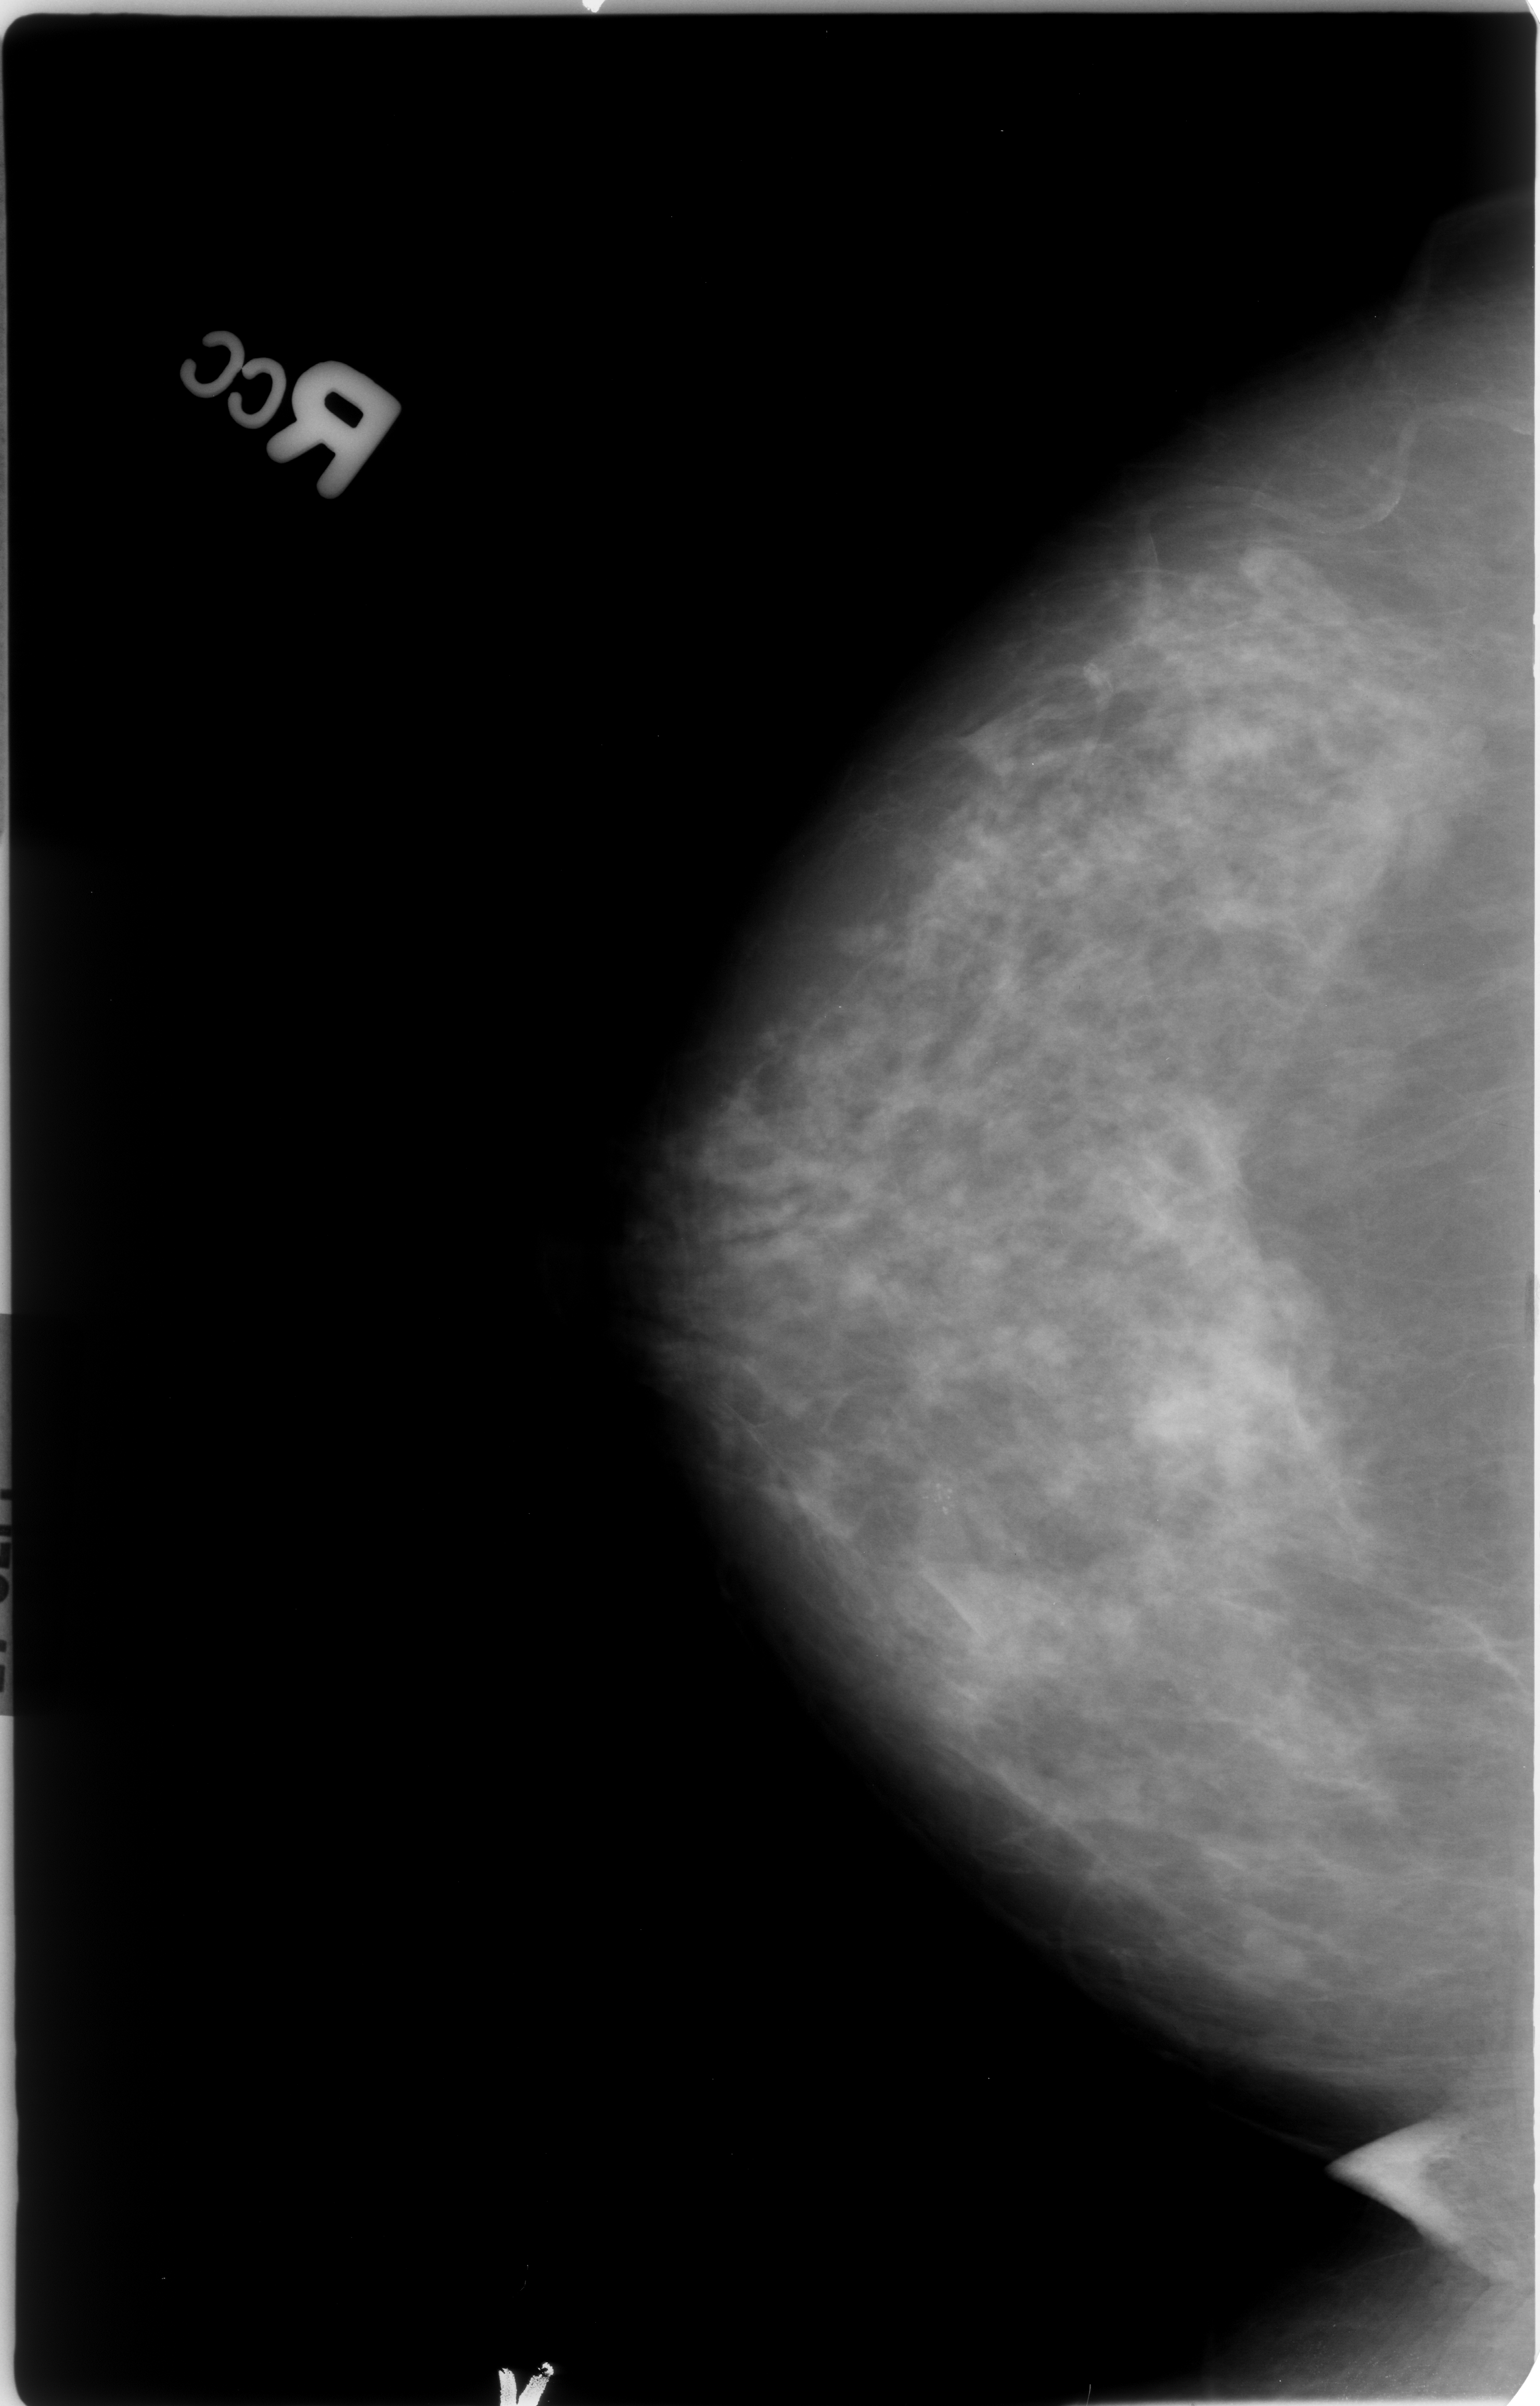
Digitized screen-film mammogram; right breast; craniocaudal (CC) view; breast composition: heterogeneously dense (BI-RADS density category 3 of 4); 1540 × 2406 image matrix.
Expert-marked regions of interest on this image (one box per marked abnormality):
- calcifications, morphology pleomorphic, distribution clustered; BI-RADS assessment category 4; subtlety rating 3 on a 1 (subtle) to 5 (obvious) scale; pathology result (as recorded, not read from the image): malignant: bounding box (x1, y1, x2, y2) in pixels: (894, 1444, 987, 1533)